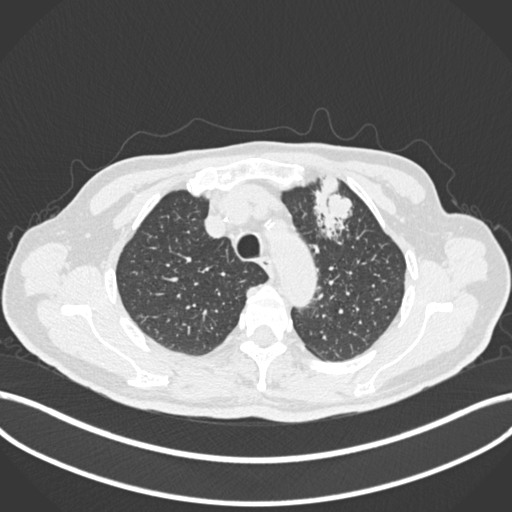
Chest CT, one axial slice. Reconstruction kernel B30f. Lung window (W 1500 / L -600 HU). 1 mm slice thickness. 512 × 512 image matrix. Patient: male, 74 years. Case-level facts recorded for this patient, not image findings: clinical TNM (as recorded): T2b N0 M1c.
Structures marked on this image (bounding box drawn by a radiologist):
- lung tumour (recorded histology: adenocarcinoma): box from (x=311, y=174) to (x=358, y=242) px